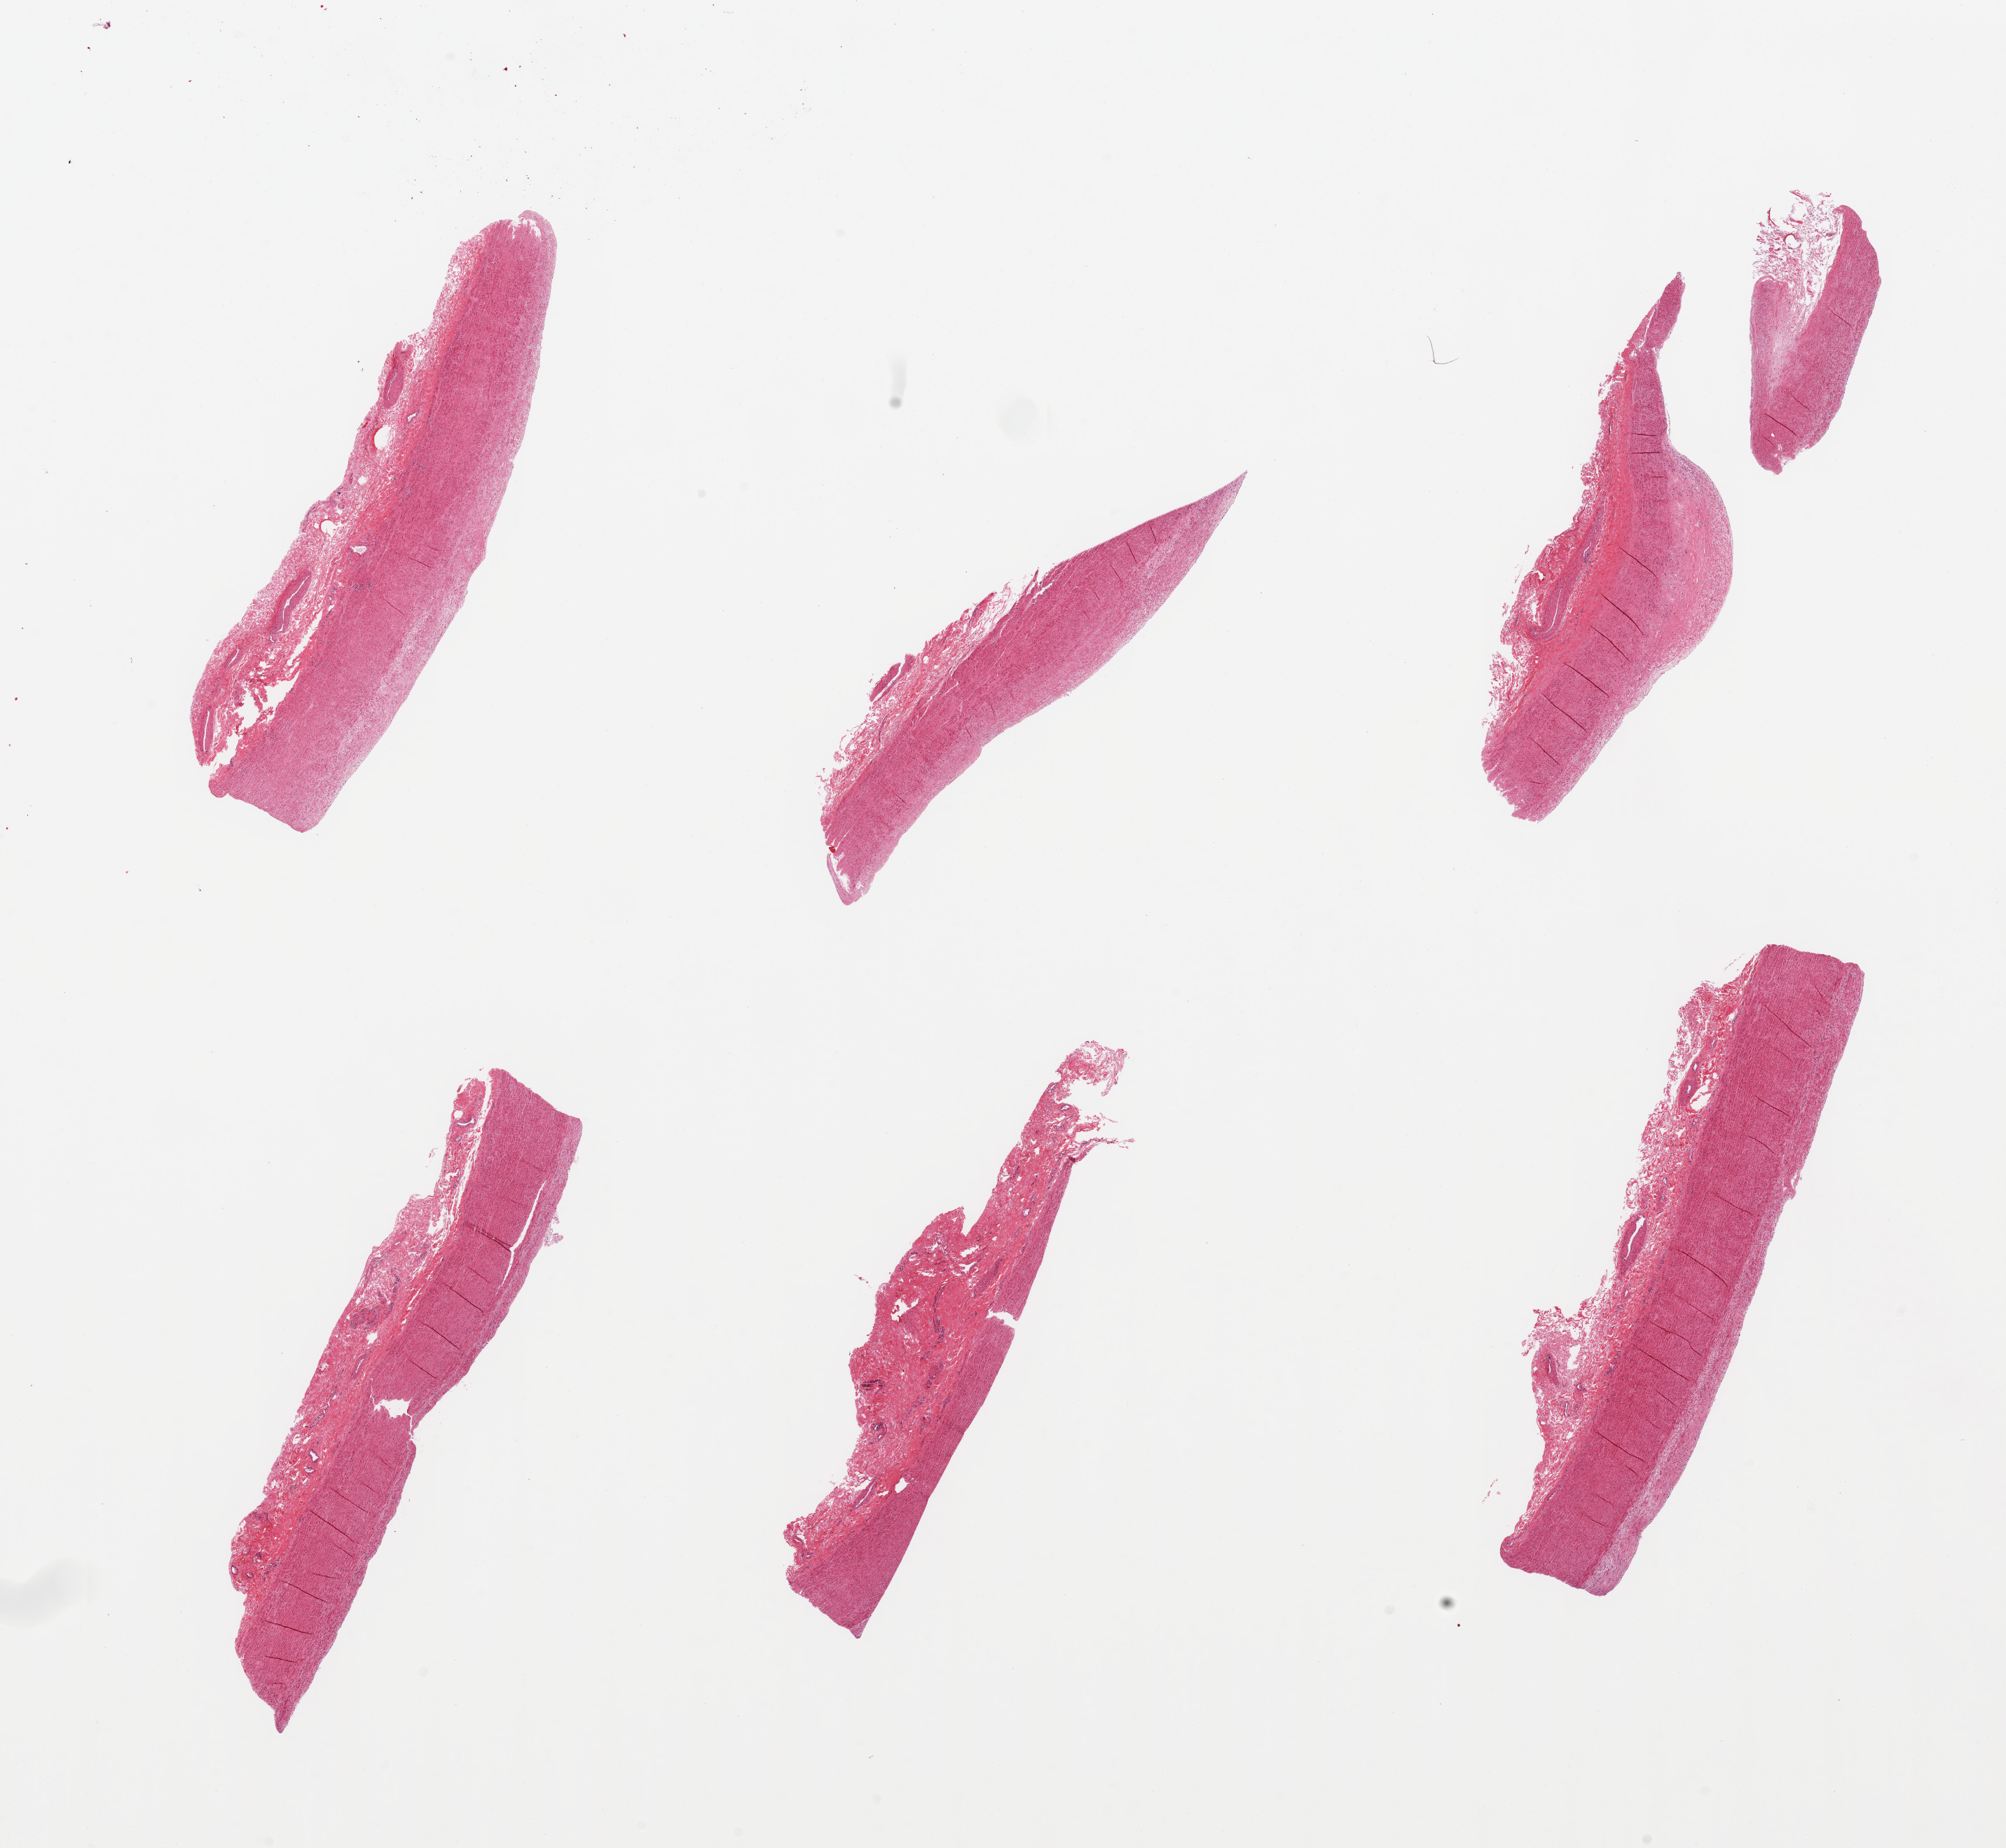
Whole-slide image, hematoxylin and eosin (H&E) stain, brightfield — a low-resolution overview of the entire scanned area, about 22.6 x 20.9 mm; PAXgene-fixed, paraffin-embedded tissue; sampled site (target tissue): aorta; tissue donor sample. Donor: male.
Review note (as recorded): 6 pieces; fibrous intimal plaques of variable thickness.